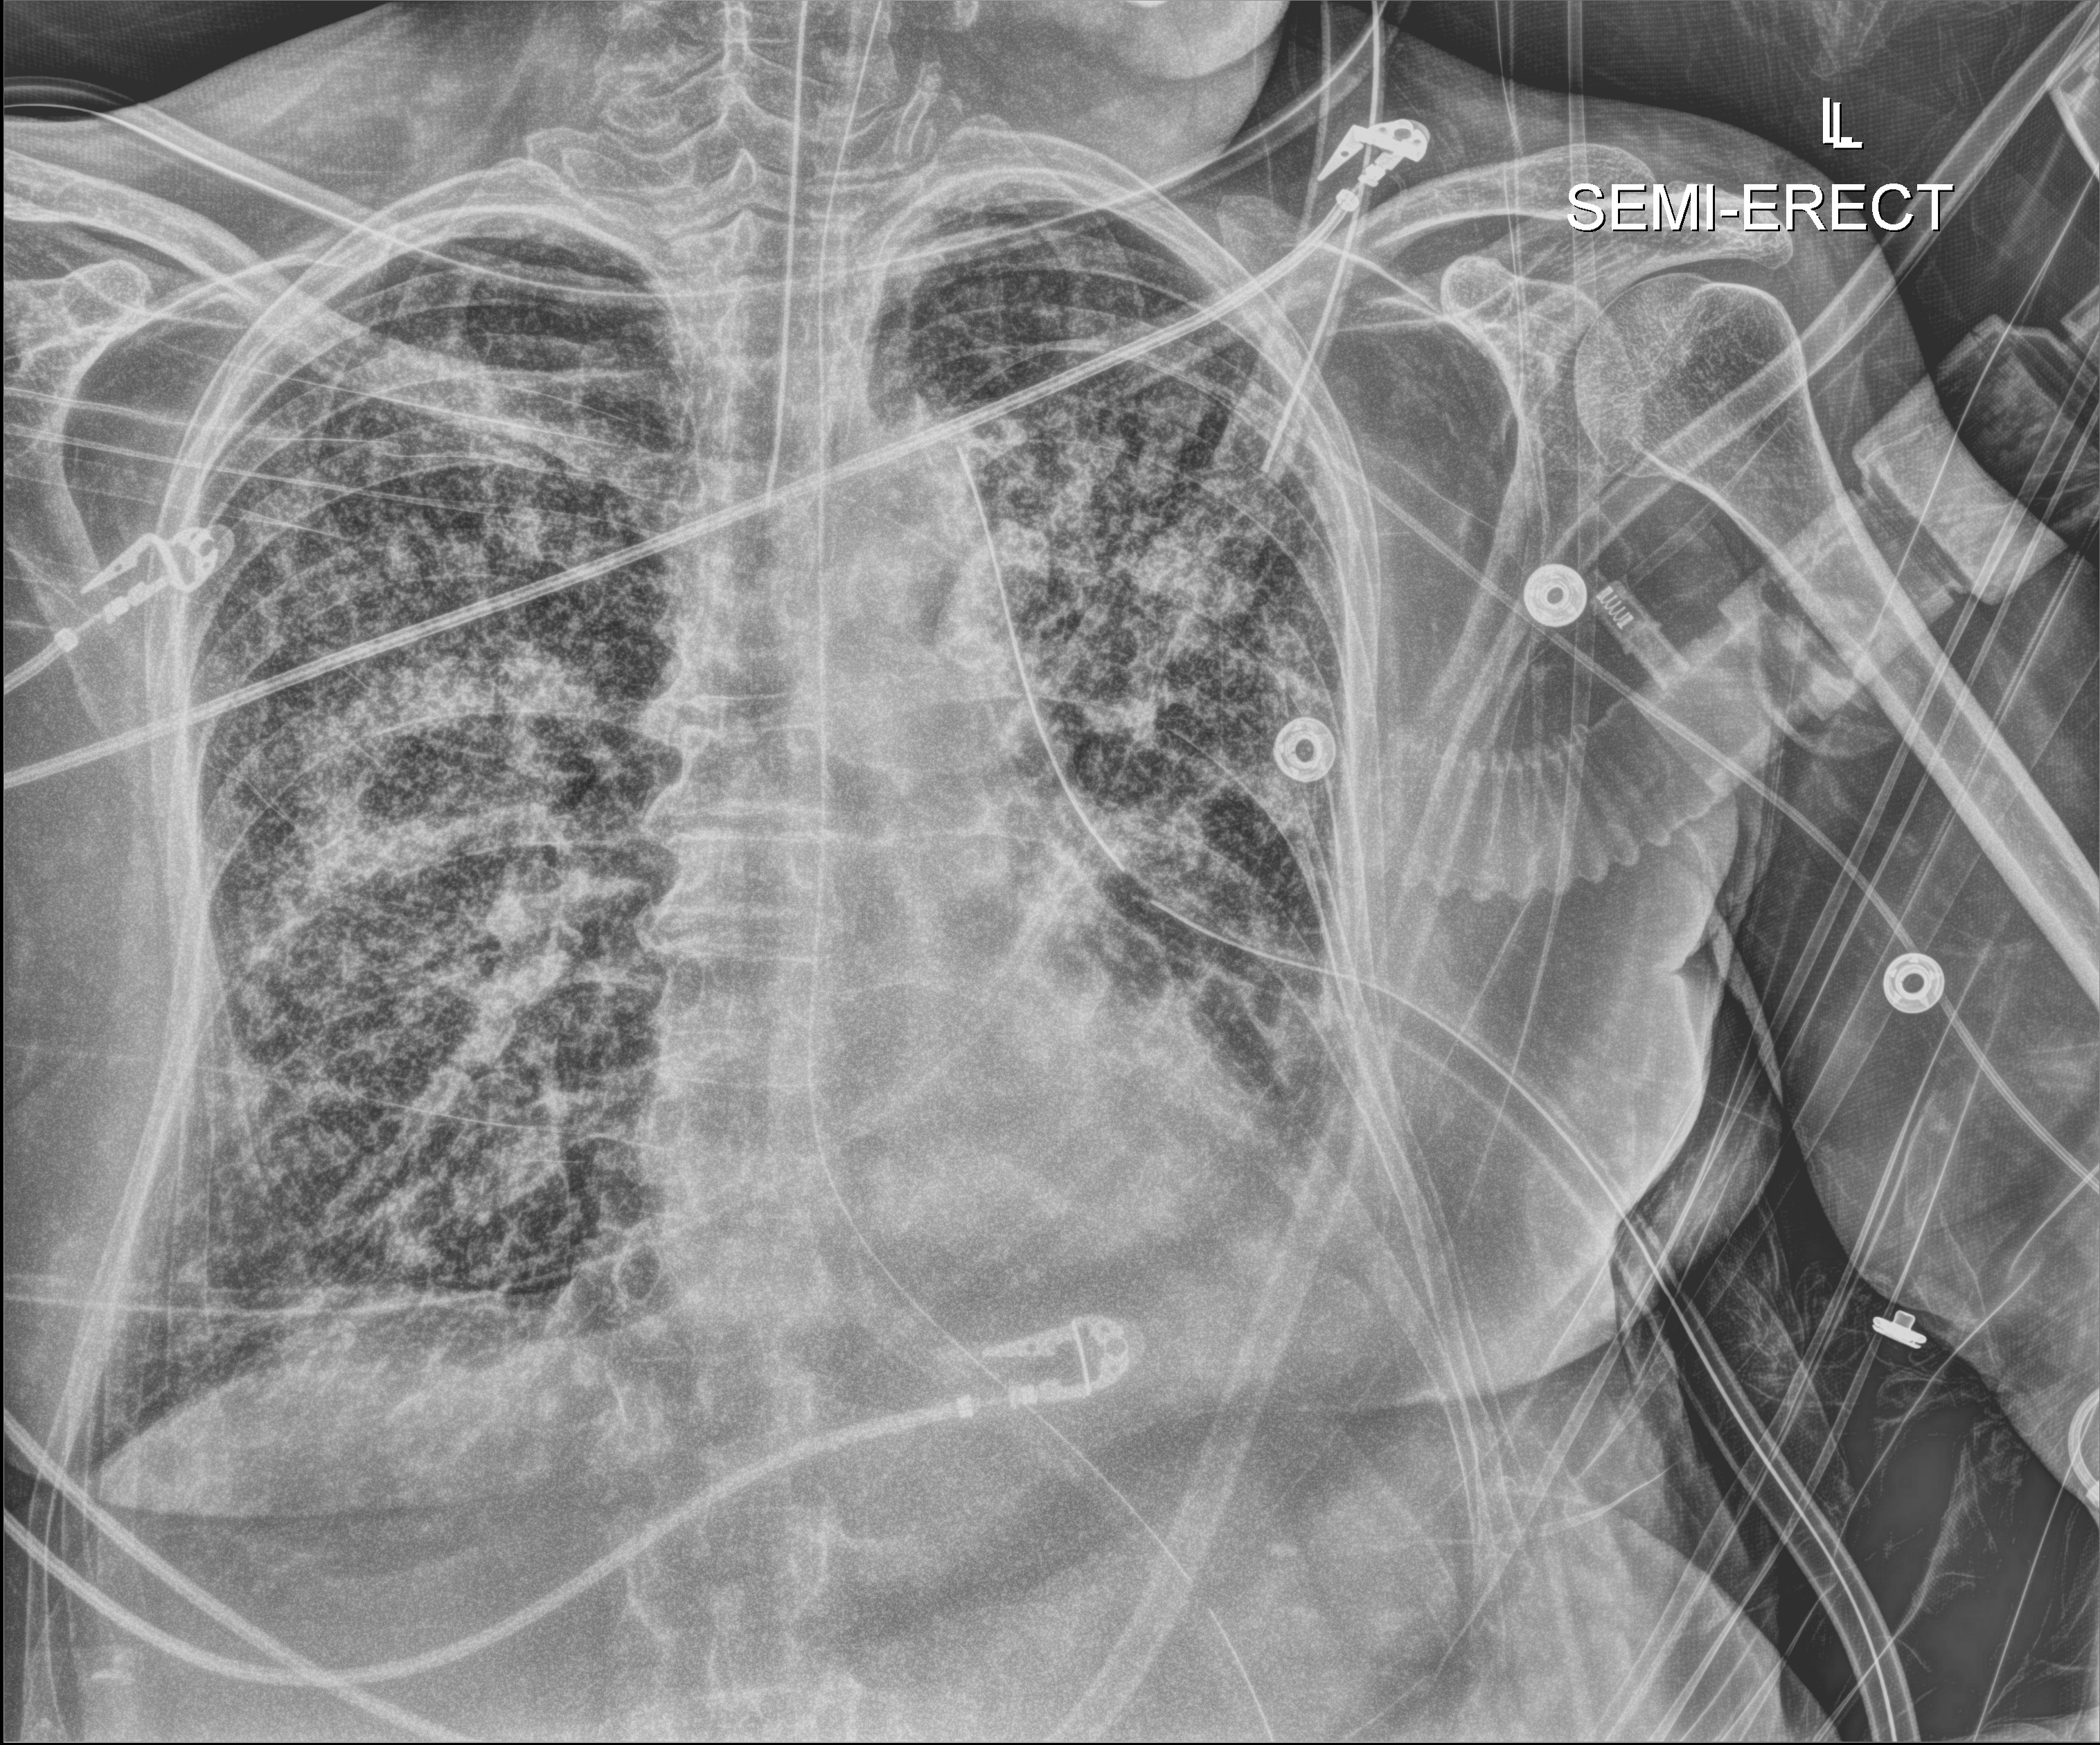
Bedside chest radiograph (digital radiography), anteroposterior (AP) projection. Female patient hospitalised with COVID-19, age 75–90 years.
From the hospital-stay record, not from the radiograph (when in the stay this image was taken is not recorded):
- mechanically ventilated during this hospital stay: yes
- admitted to intensive care during this hospital stay: yes
- length of hospital stay: 70 days